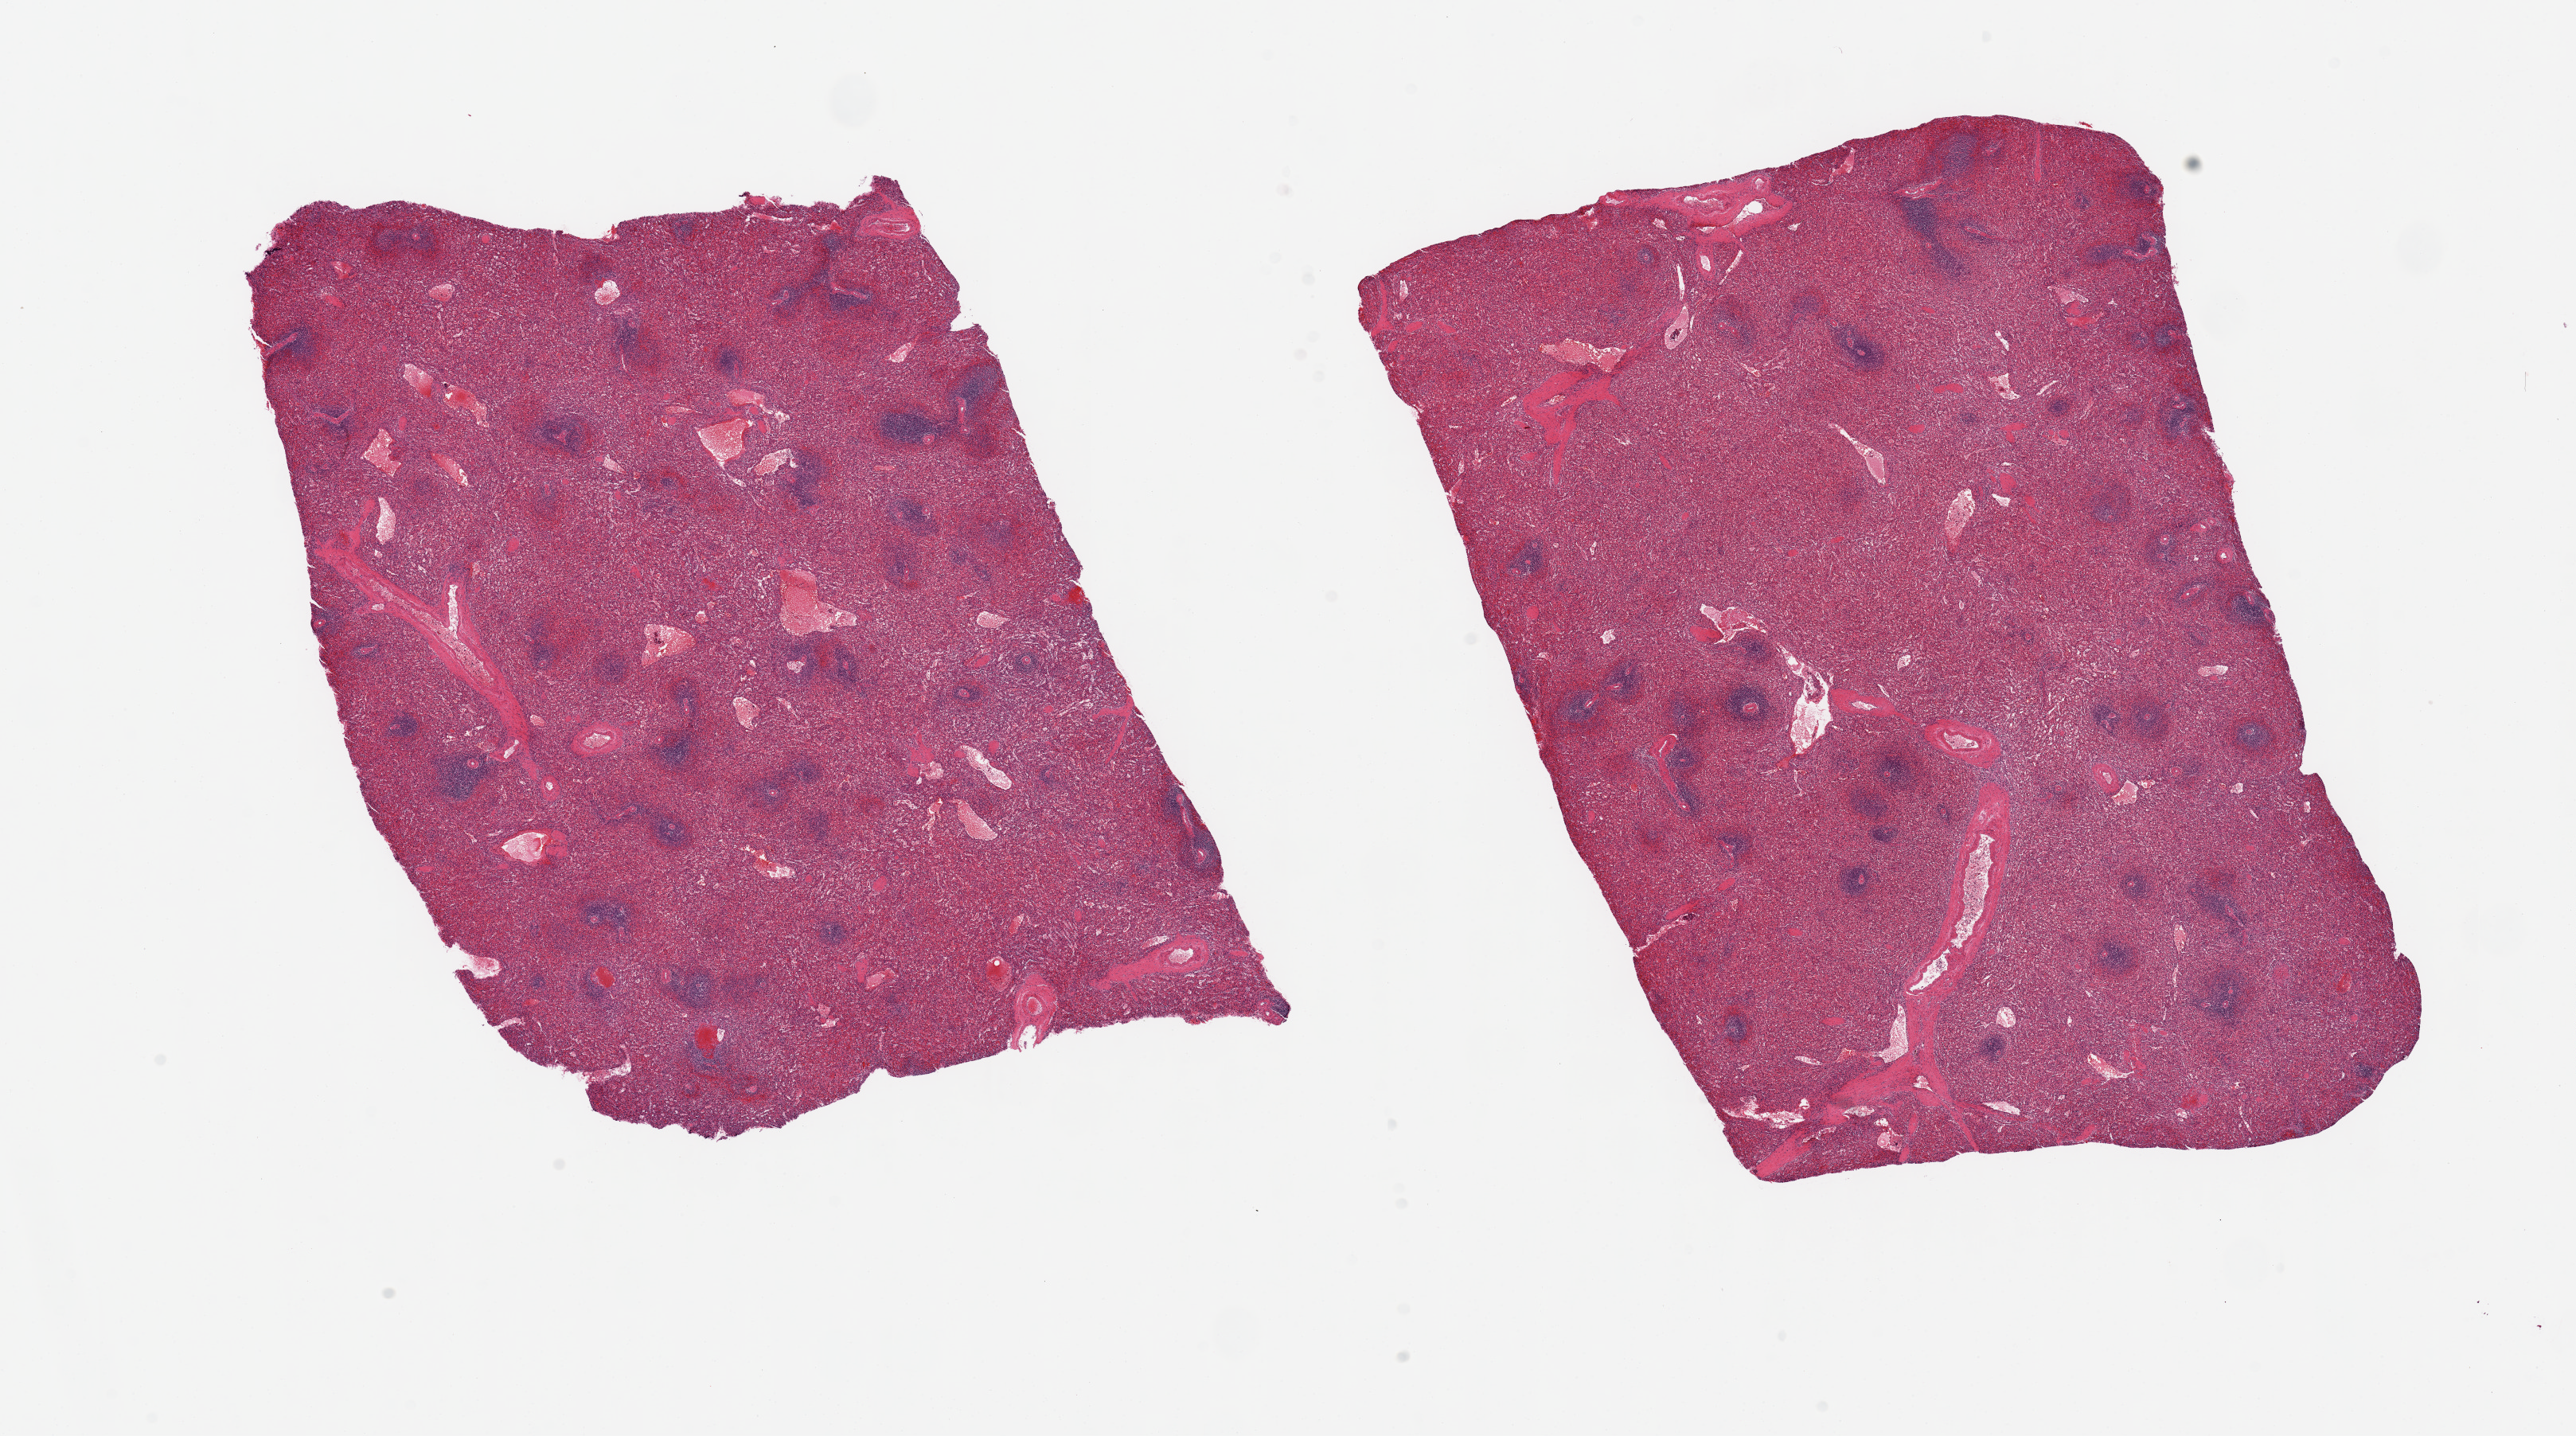
Digitized hematoxylin and eosin (H&E)-stained section — low-resolution overview of the scanned area, about 25.6 x 14.3 mm (from a 20x scan). PAXgene-fixed paraffin-embedded (PFPE) section. Sampled site (target tissue): spleen. Tissue donor sample. Donor: male.
Review note (as recorded): 2 pieces, minimal congestion.